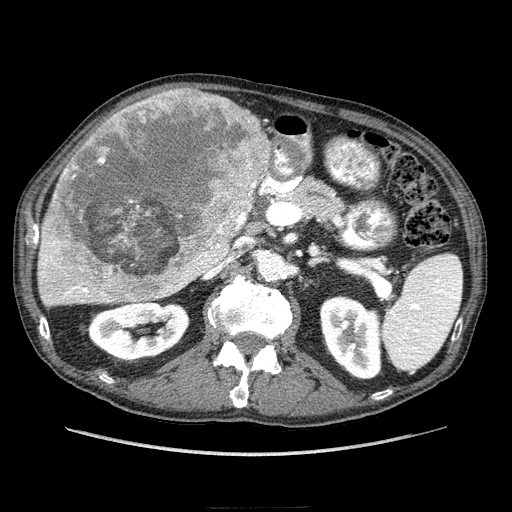
Contrast-enhanced abdominal CT (liver protocol), one axial slice; position 127 of 218 along the scan axis; reconstruction kernel STANDARD; 100 kVp; soft-tissue window (W 400 / L 40 HU); 2.5 mm slice thickness; 512 × 512 image matrix. Case-level facts recorded for this patient, not image findings: diagnosis: hepatocellular carcinoma (patient treated with transarterial chemoembolisation; whether this scan precedes or follows treatment is not stated here); TNM stage (as recorded): Stage-IIIA; Child-Pugh class: A; tumour nodularity: multinodular.
Outlined on this slice (semi-automatically segmented with operator editing):
- liver parenchyma outside the tumour (the mass and vessels are separate outlines, so this box may not span the whole liver): bounding box (x1, y1, x2, y2) in pixels: (38, 98, 270, 306)
- mass: (41, 83, 273, 300)
- liver vessels: (41, 218, 246, 301)